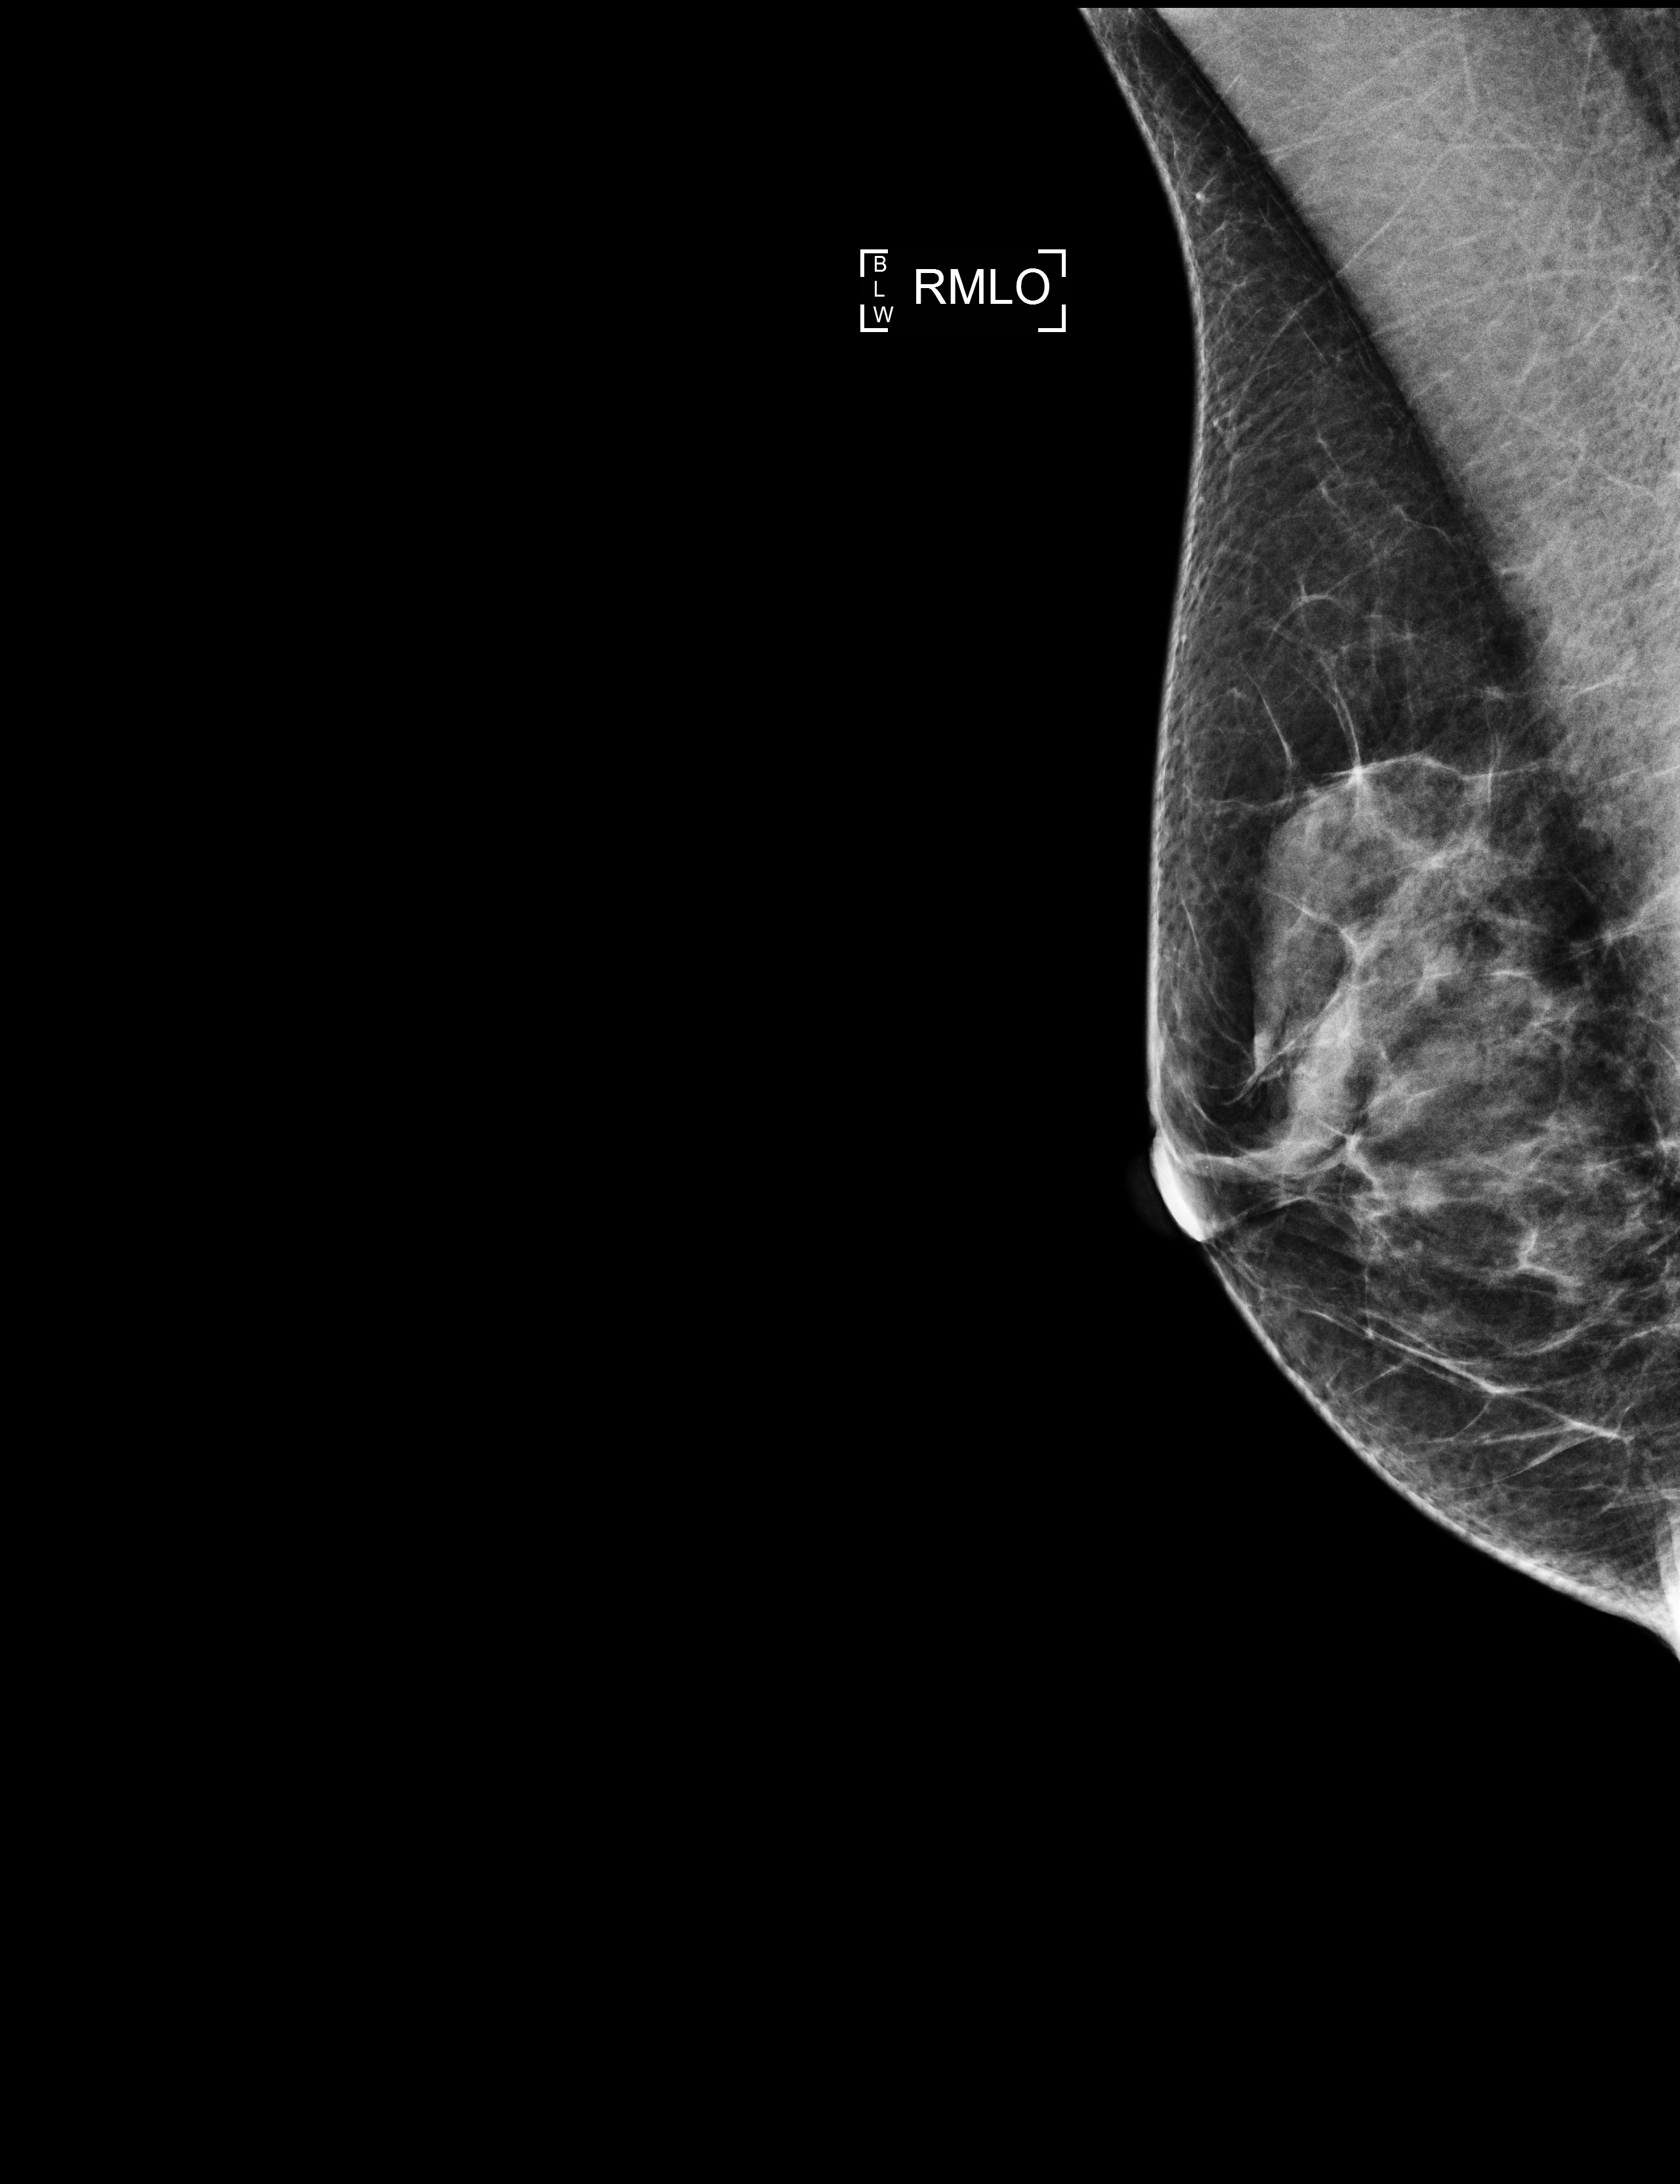
Annual screening mammography examination; system: Selenia Dimensions. Female patient, age 58 years.
Image type: full-field digital mammogram. Breast: right. Projection: medio-lateral oblique projection.